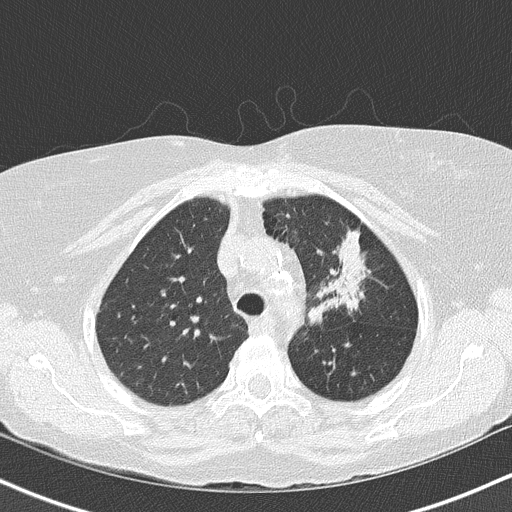
Axial slice from a low-dose chest CT screening exam. Third screening round (two years after baseline). Lung window (W 1500 / L -600 HU). 2 mm slice thickness. Lung (sharp) reconstruction kernel (B50f). 120 kVp. 512 × 512 image matrix. Female, age 68 years at enrolment. Former smoker at enrolment.
Expert reader's lesion annotation, bounding box (x1, y1, x2, y2) in pixels: (298, 217, 382, 325). Reader record for this screening exam (exam-level; its link to the box is not recorded): non-calcified nodule or mass ≥4 mm, left upper lobe, 5 × 5 mm, poorly defined margins, mixed attenuation, pre-existing on the prior screen: yes; interval growth: yes.